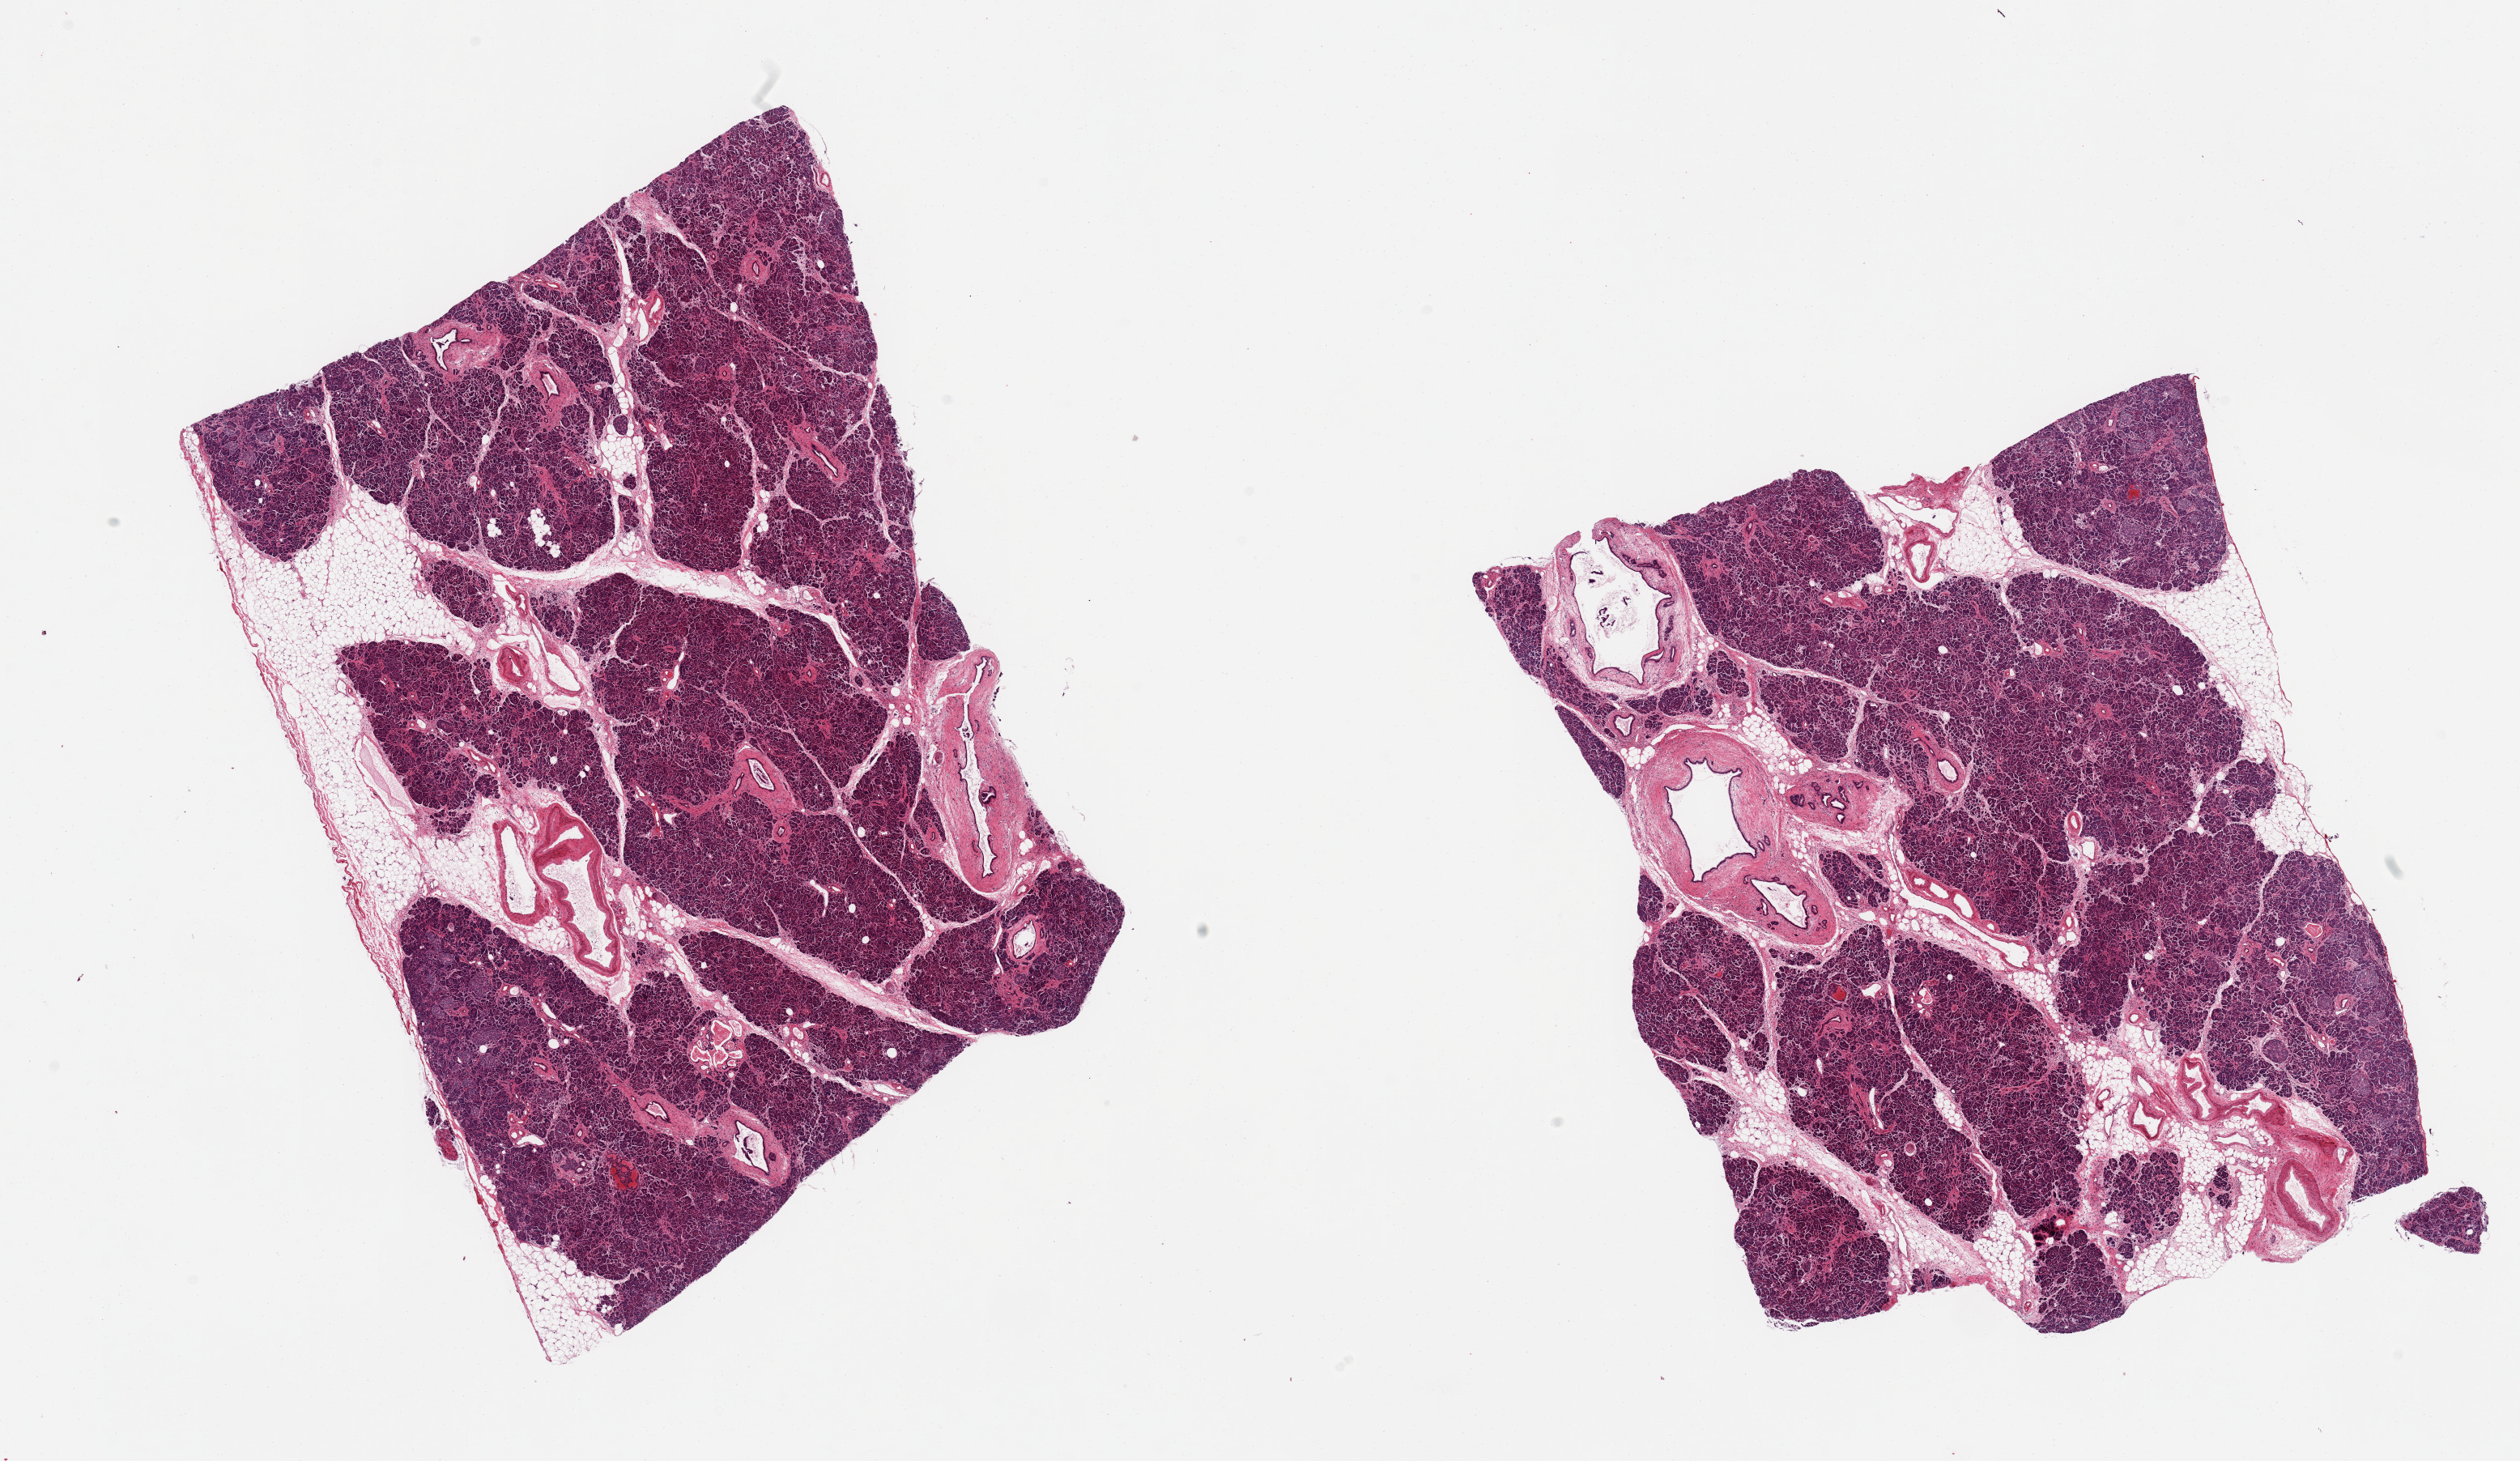
Digitized haematoxylin and eosin-stained section, brightfield — shown as a low-resolution overview of the whole scanned area (about 24.6 x 14.3 mm). PAXgene-fixed paraffin-embedded (PFPE) section. Section of pancreas (target tissue). Donor tissue sample. Donor: male.
- pathologist's review note for this sample: 2 pieces; 10% internal fibrofatty component